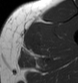
MRI of an extremity soft-tissue mass, one axial slice. Position 32 of 43 along the scan axis. MR volume resampled by the dataset authors to the PET/CT grid (not the native acquisition matrix). 3.27 mm slice thickness. 78 × 83 image matrix, field of view 76 × 81 mm. Male patient. Case-level facts recorded for this patient, not image findings: histological type: pleiomorphic leiomyosarcoma; grade: high; site of the primary tumour: left thigh.
Structures marked on this image (expert contour drawn on MRI and transferred to this co-registered scan by the dataset authors):
- gross tumour volume including surrounding oedema: bounding box [x1, y1, x2, y2] px = [20, 26, 44, 57]